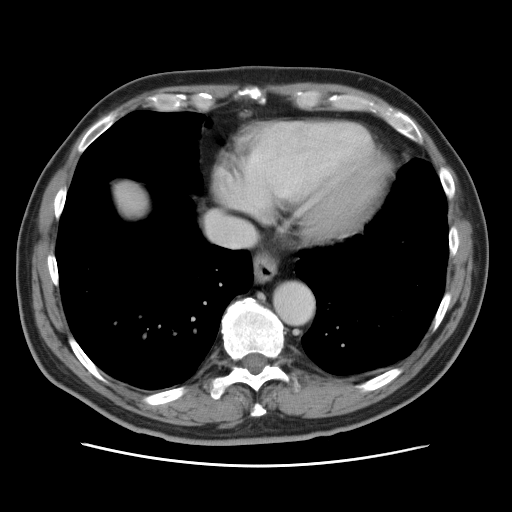
Contrast-enhanced abdominal CT, one axial slice. Position 75 of 80 along the scan axis. 120 kVp. Intravenous contrast given. Soft-tissue window (W 400 / L 40 HU). 5 mm slice thickness. 512 × 512 image matrix, field of view 370 × 370 mm. Male patient, age 69 years. From the clinical record (not read from this slice): diagnosis: colorectal cancer liver metastases, imaged before liver resection; multiple liver metastases: no.
Annotated regions visible in this slice (manually delineated by an expert):
- hepatic veins: bounding box <207,213,253,247> (left, top, right, bottom; pixels)
- liver: <114,183,147,216>